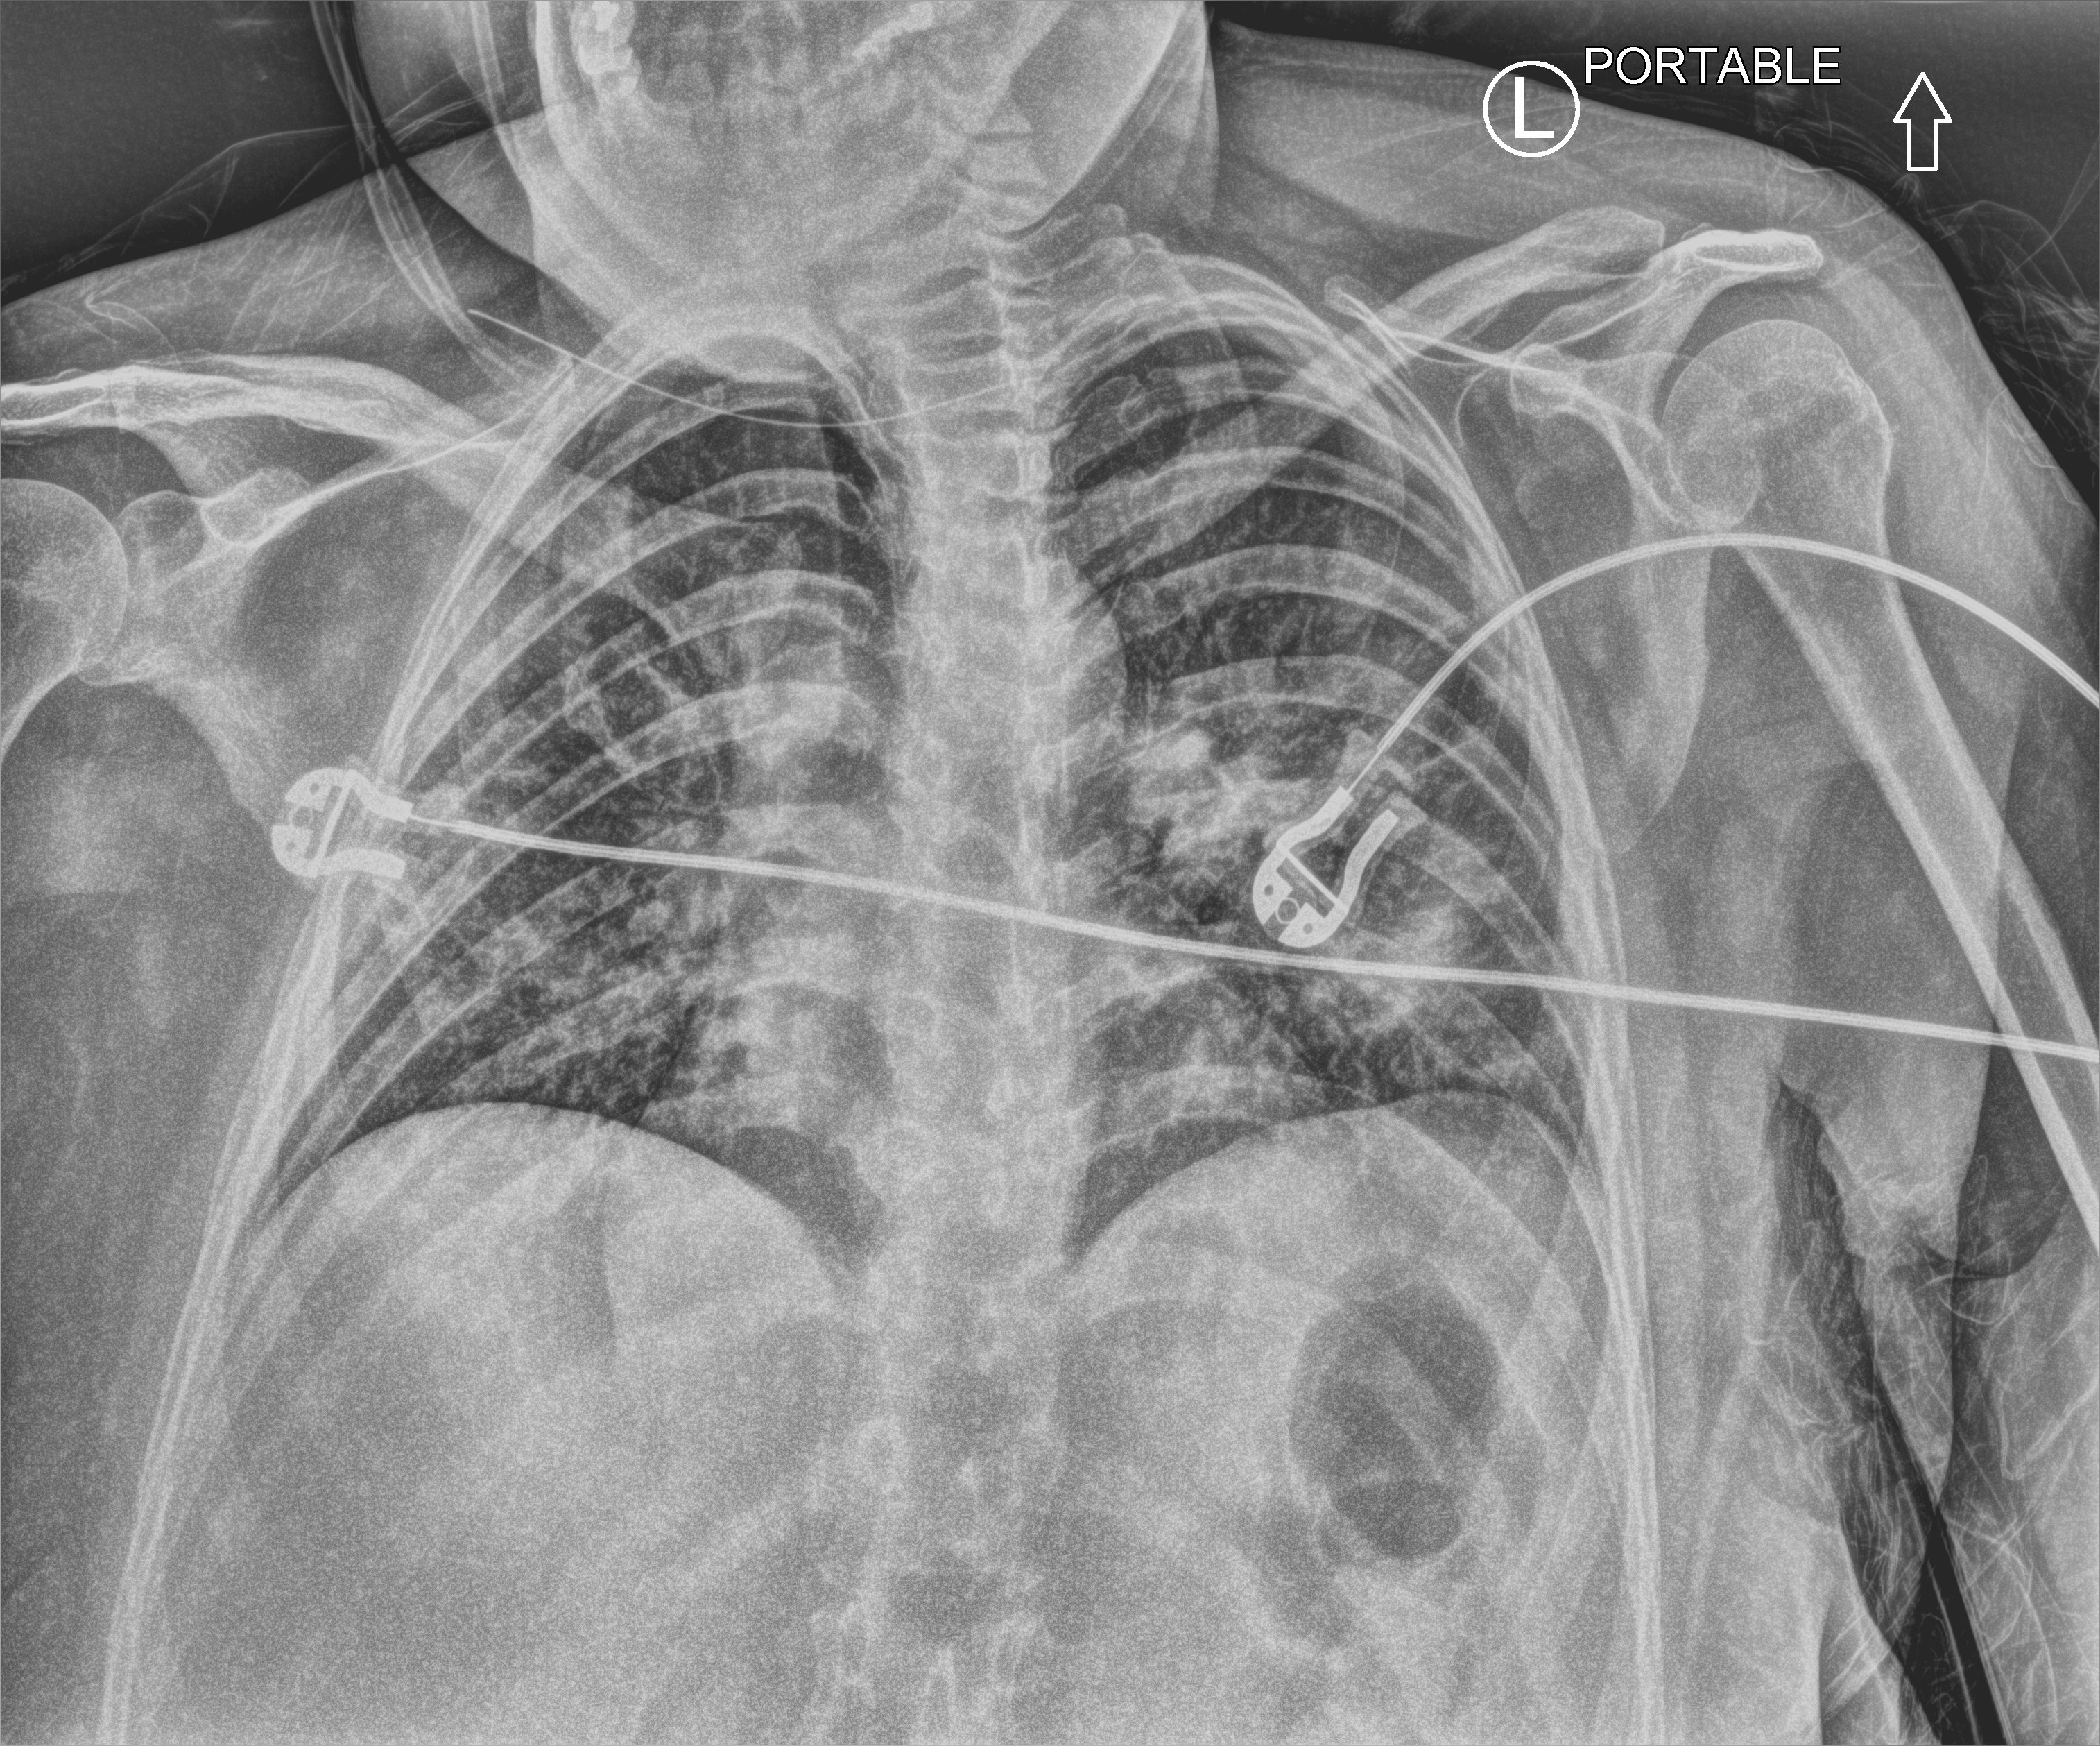
Chest X-ray (portable), anteroposterior (AP) projection. Female patient hospitalised with COVID-19, age 18–59 years.
Hospital-stay facts (about this admission, not read from this image; timing relative to this image not recorded): length of hospital stay: 6 days; mechanically ventilated during this hospital stay: no; admitted to intensive care during this hospital stay: no.